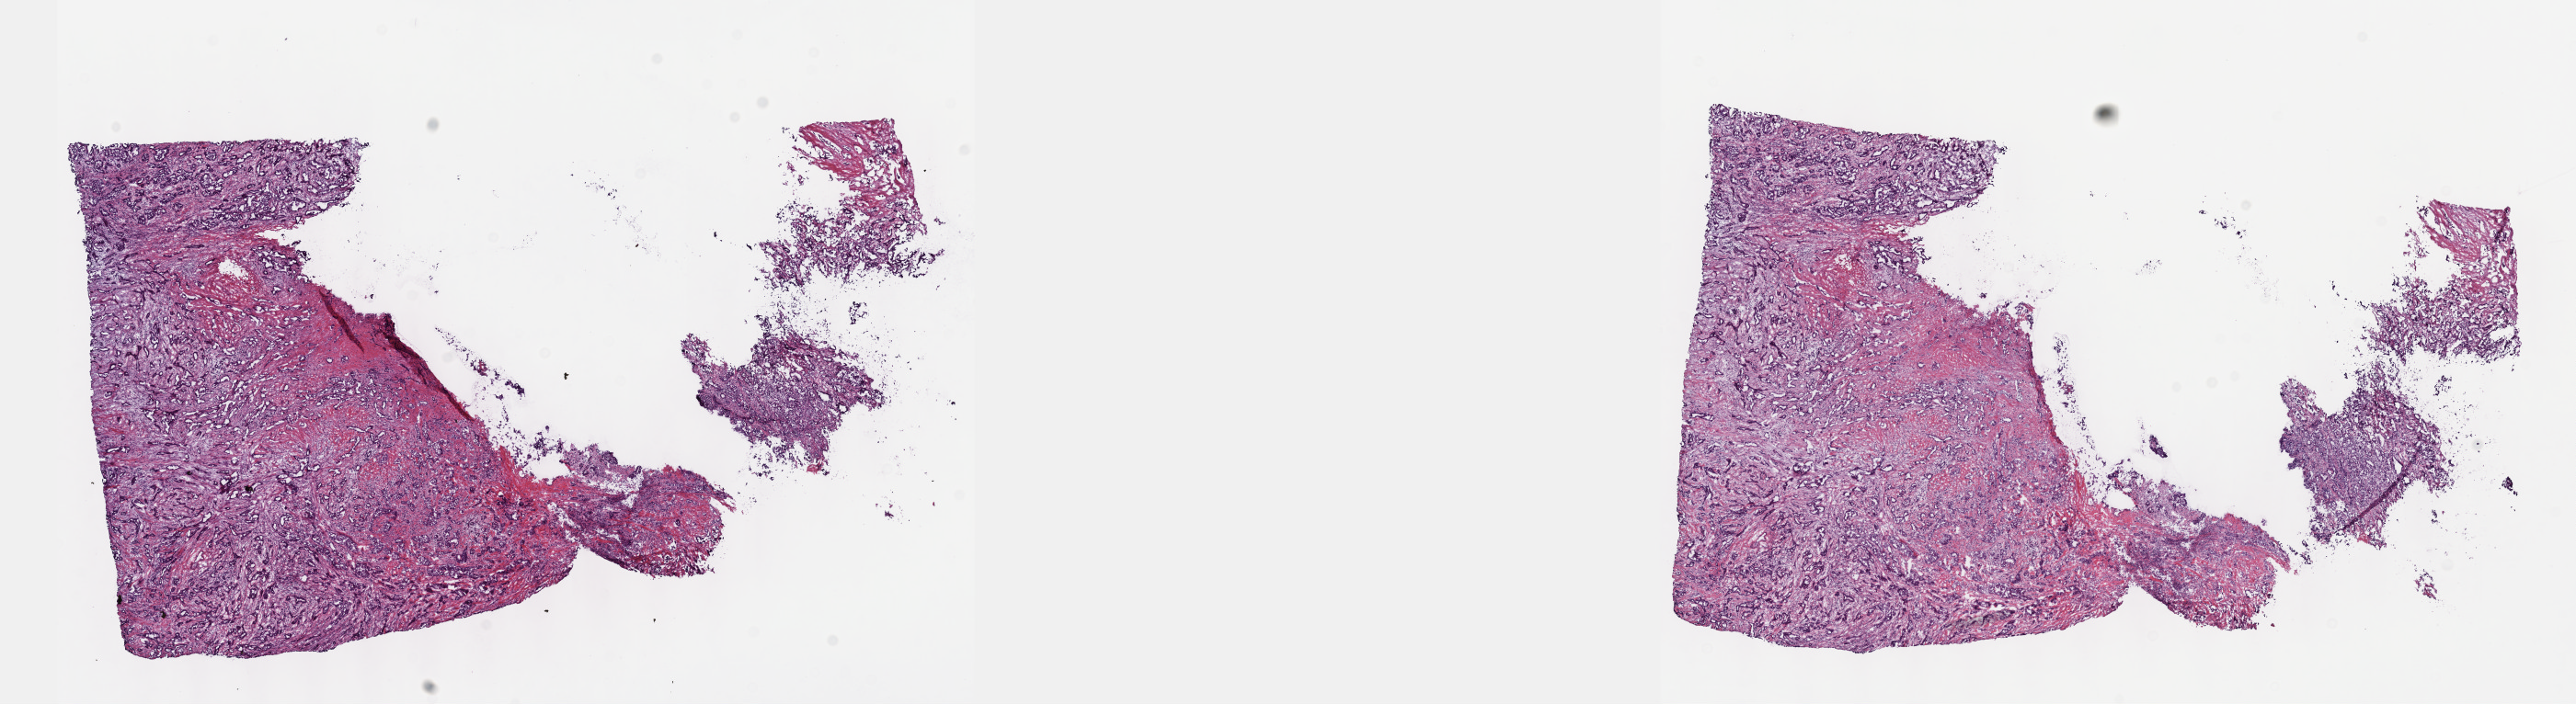
Digitized H&E tissue section (whole slide) — a low-resolution overview of the entire scanned area, about 22.6 x 6.2 mm. Pathologist review of this section (percent, as recorded): tumour cells 100%, tumour nuclei 60%, normal cells 0%, stromal cells 0%, necrosis 0%. Inflammatory infiltration, as recorded: lymphocyte infiltration 3%, monocyte infiltration 0%, neutrophil infiltration 0%.
* specimen: frozen section from the top of the tissue portion; sample: primary tumour, bile duct